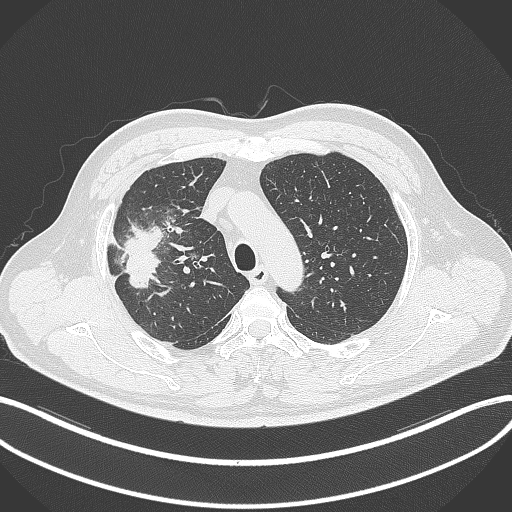
Chest CT, one axial slice; position 256 of 348 along the scan axis; 120 kVp; lung window (W 1500 / L -600 HU); 1 mm slice thickness; 512 × 512 image matrix, field of view 400 × 400 mm. Male patient, age 55 years. Case-level facts recorded for this patient, not image findings: clinical TNM (as recorded): T3 N2 M1.
Structures marked on this image (rectangle marked by the reading radiologist):
- lung tumour (recorded histology: adenocarcinoma): bounding box <120,220,162,293> (left, top, right, bottom; pixels)